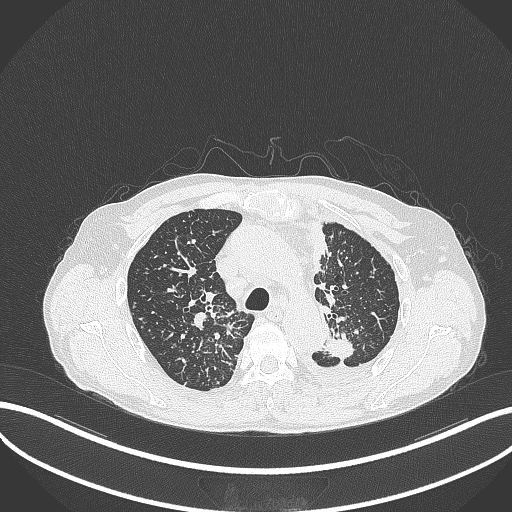
Chest CT, one axial slice. Slice 258 of 325 in the series (ordered by position). Reconstruction kernel B70f. 120 kVp. Lung window (W 1500 / L -600 HU). 512 × 512 image matrix, field of view 400 × 400 mm. Patient: male, 58 years. From the clinical record (not read from this slice): clinical TNM (as recorded): T1c N3 M1.
Annotated regions visible in this slice (bounding box drawn by a radiologist):
- lung tumour (recorded histology: adenocarcinoma): box from (x=323, y=329) to (x=357, y=360) px